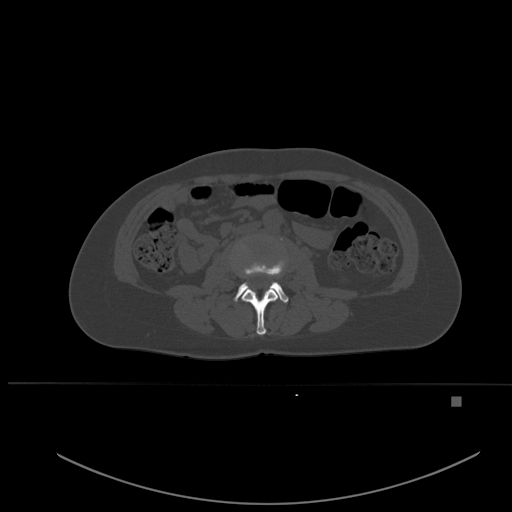
CT including the spine, one axial slice. Position 203 of 651 along the scan axis. Bone window (W 1800 / L 400 HU). 1.5 mm slice thickness. 512 × 512 image matrix, field of view 443 × 443 mm. Female patient, age 49 years. From the clinical record (not read from this slice): primary cancer: breast.
Outlined on this slice (semi-automatic segmentation, software-assisted and operator-edited):
- L2 vertebra: bounding box [x1, y1, x2, y2] px = [242, 263, 278, 335]
- L3 vertebra: [234, 262, 288, 303]